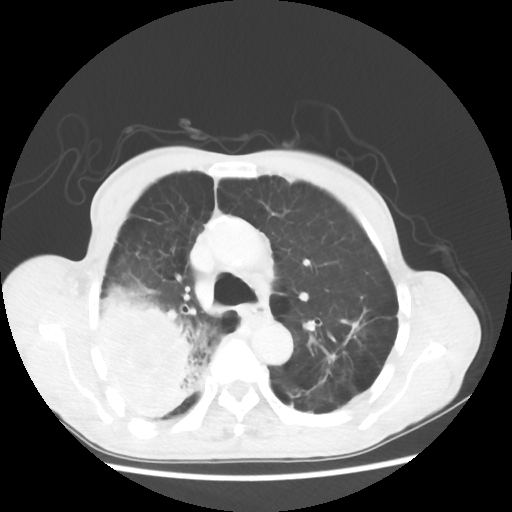
Chest CT, one axial slice. Position 37 of 58 along the scan axis. 100 kVp. Lung window (W 1500 / L -600 HU). 5 mm slice thickness. 512 × 512 image matrix, field of view 351 × 351 mm. Patient: male, 75 years. Case-level facts recorded for this patient, not image findings: clinical TNM (as recorded): T4 N1 M1.
Structures marked on this image (bounding box drawn by a radiologist):
- lung tumour (recorded histology: adenocarcinoma): bounding box [x1, y1, x2, y2] px = [88, 282, 207, 421]